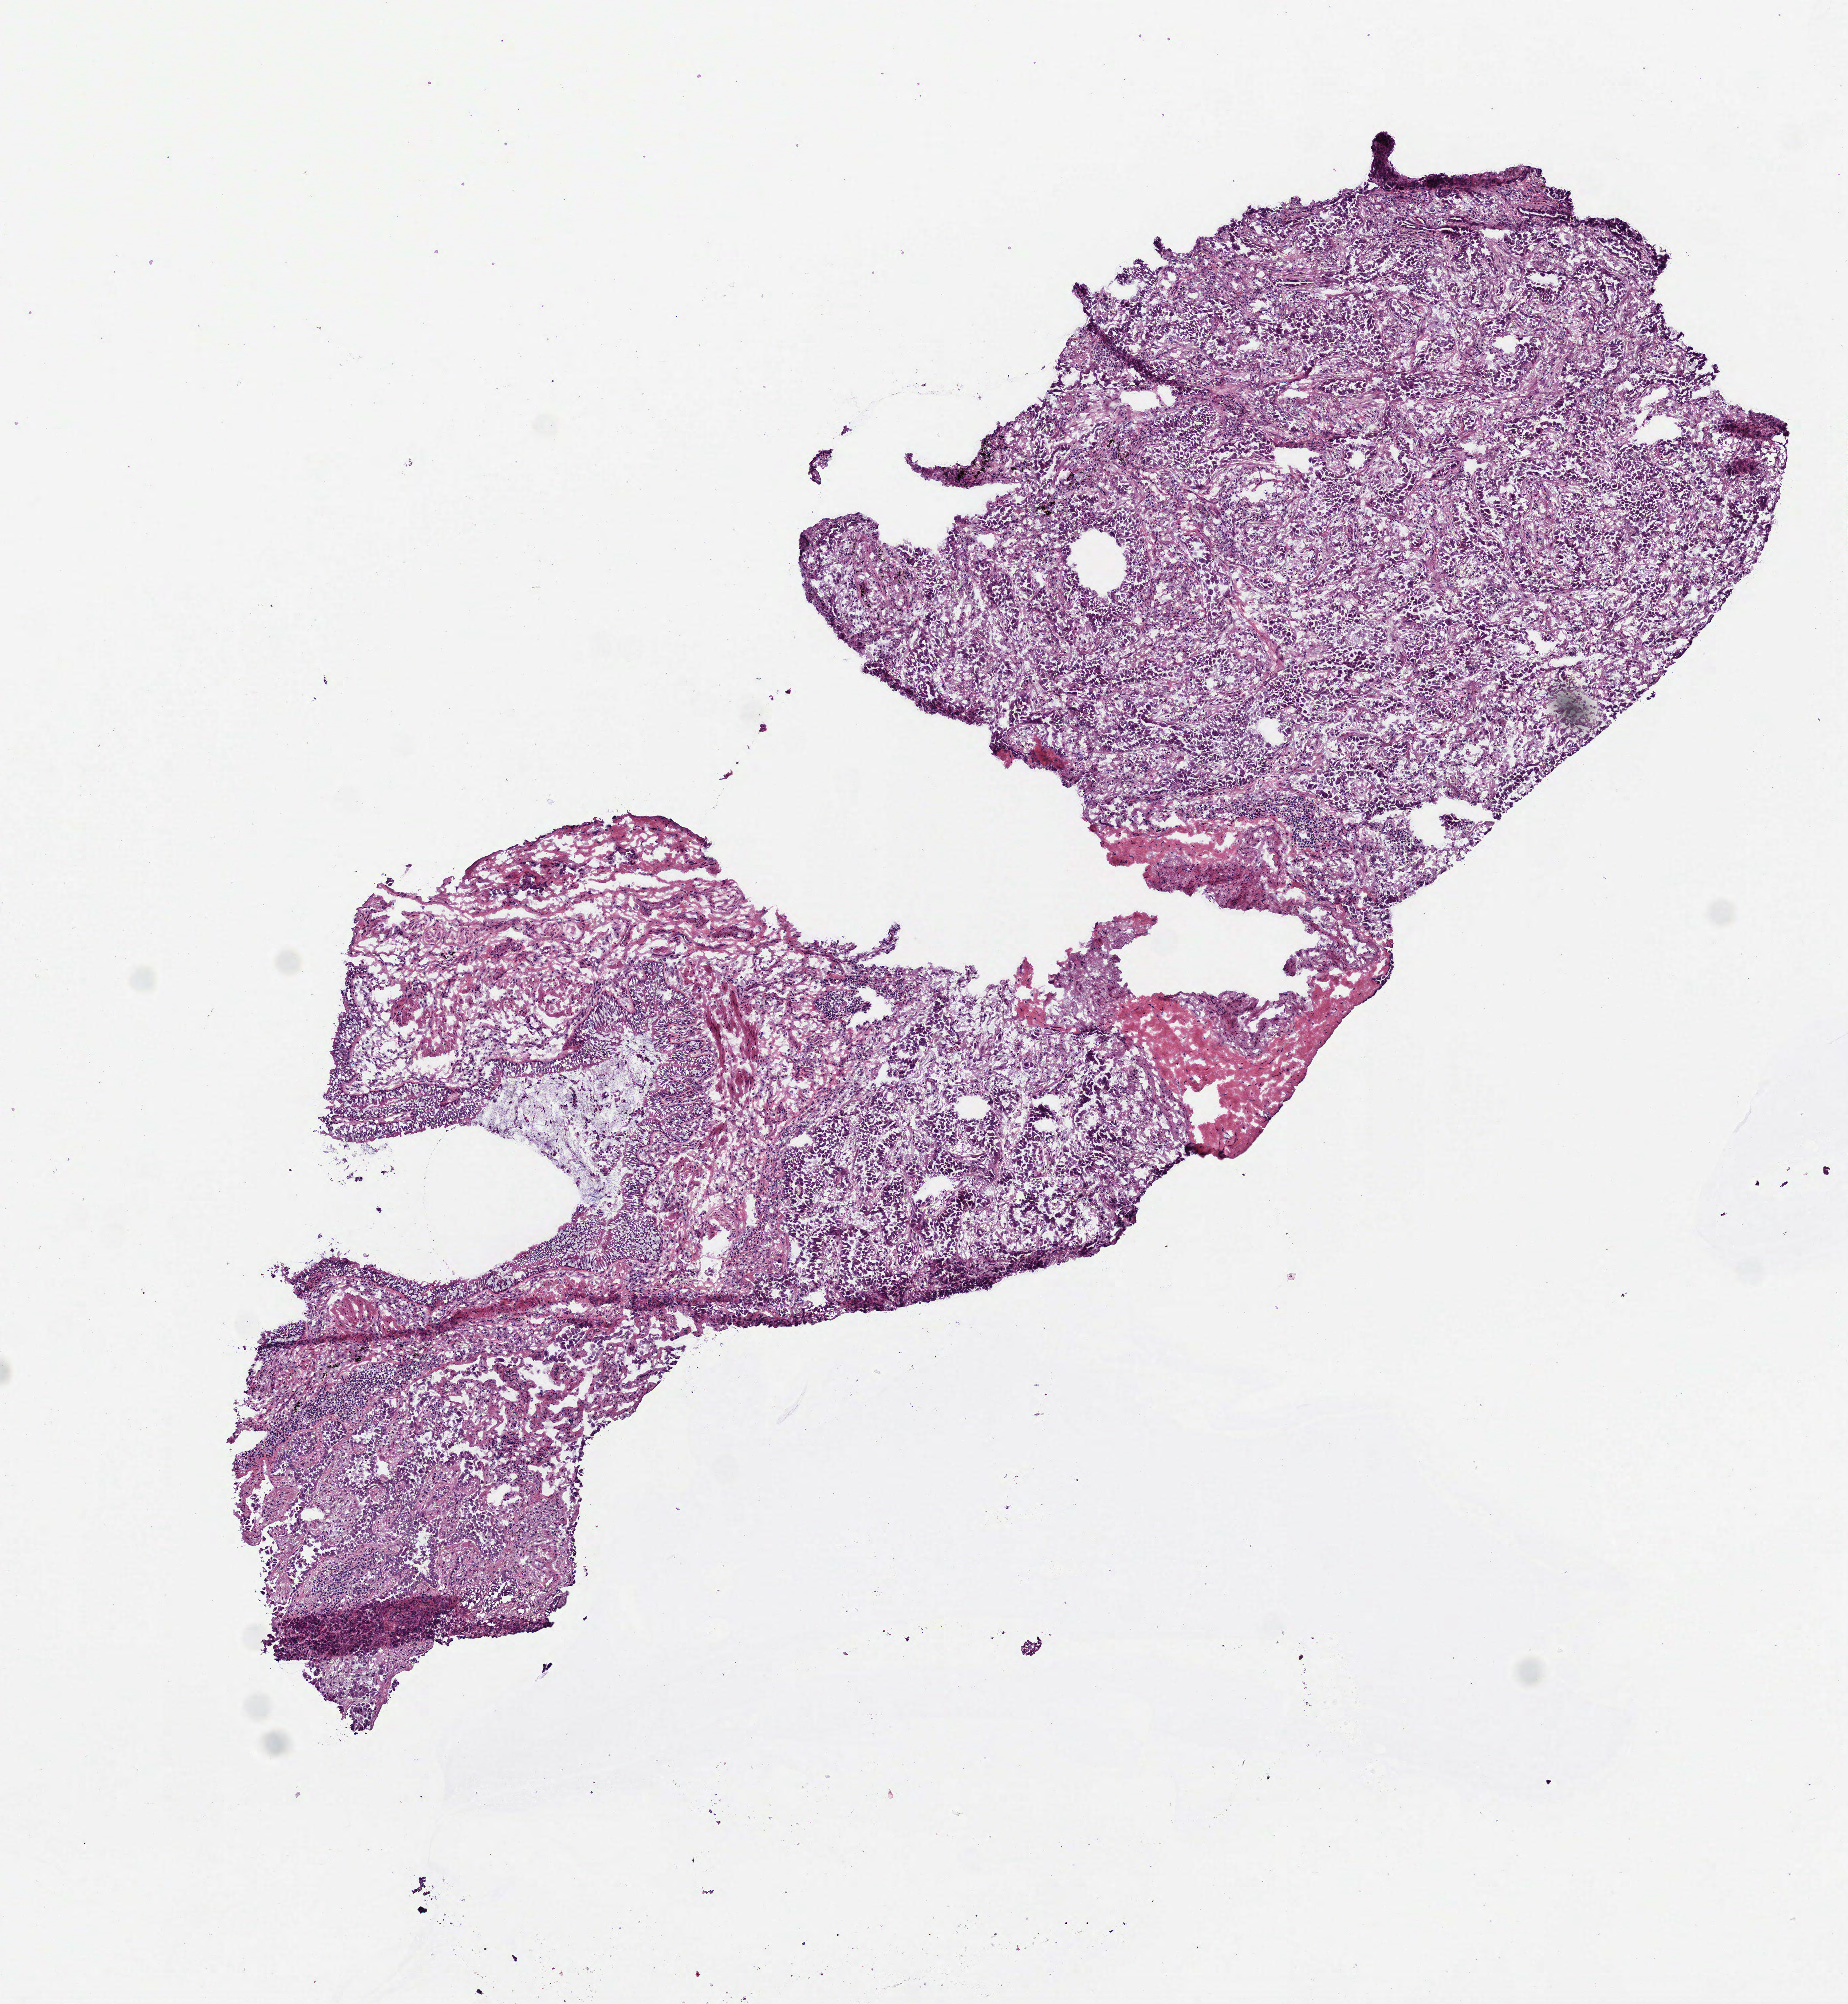
Digitized H&E tissue section (whole slide) — low-resolution overview of the scanned area, about 5.6 x 6.0 mm. Frozen section from the top of the tissue portion. Lung, primary tumour sample. Male patient. Pathologist review of this section (percent, as recorded): tumour cells 78%, tumour nuclei 80%, normal cells 5%, stromal cells 15%, necrosis 2%.
Pathologic diagnosis: Adenocarcinoma, NOS (upper lobe, lung). TNM: T2 N0 M0. AJCC pathologic stage: IB (6th edition).